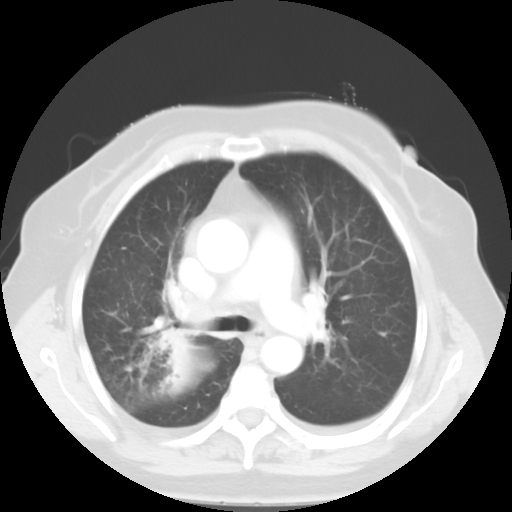
Chest CT, one axial slice. Slice 34 of 52 in the series (ordered by position). Reconstruction kernel STANDARD. 120 kVp. Lung window (W 1500 / L -600 HU). 512 × 512 image matrix. Patient: female, 81 years. From the clinical record (not read from this slice): clinical TNM (as recorded): T4 N3 M1b.
Structures marked on this image (bounding box drawn by a radiologist):
- lung tumour (recorded histology: adenocarcinoma): box from (x=146, y=319) to (x=197, y=388) px